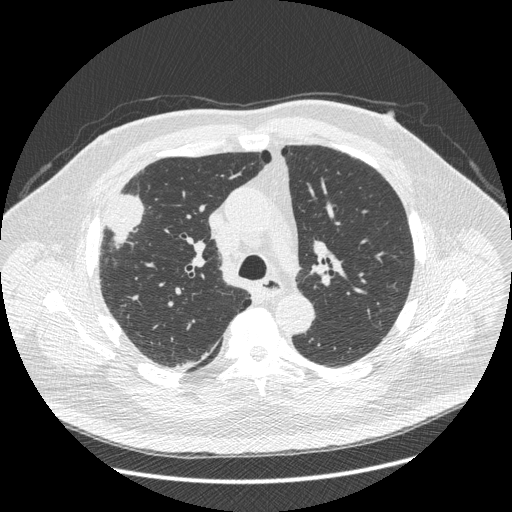
Chest CT (low-dose screening protocol), one axial image. Third screening round (two years after baseline). Lung window (W 1500 / L -600 HU). 1.25 mm slice thickness. Standard (soft-tissue) reconstruction kernel (STANDARD). Slice 141 of 426 in the series. 512 × 512 image matrix, field of view 400 × 400 mm. Male, age 66 years at enrolment. Current smoker at enrolment.
Expert reader's lesion annotation, bounding box <86,189,145,266> (left, top, right, bottom; pixels). Screening reader's record for this exam (one nodule recorded; not confirmed to be the boxed lesion): non-calcified nodule or mass ≥4 mm, right upper lobe, 48 × 25 mm, spiculated (stellate) margins, soft tissue attenuation, pre-existing on the prior screen: no.